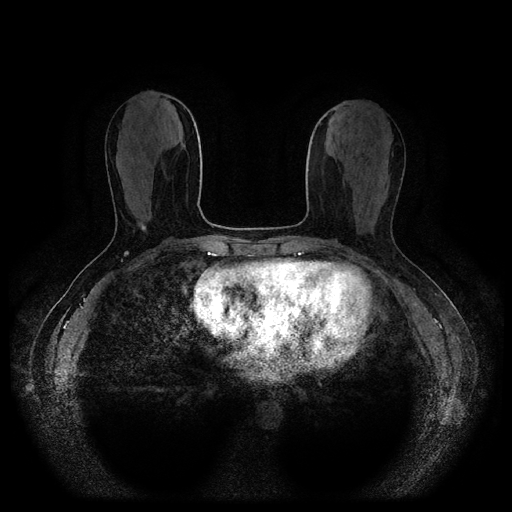
Breast MRI (dynamic contrast-enhanced, multi-phase), one axial slice. Slice 37 of 116 in the series (ordered by position). Dynamic contrast-enhanced series, time point 2 of 5 at this slice position (early post-contrast). 1.5 T. TE 2.6 ms, TR 5.3 ms. 2 mm slice thickness. 512 × 512 image matrix, field of view 360 × 360 mm. Patient: female, 53 years.
Structures marked on this image (semi-automatically segmented with operator editing):
- breast lesion (labelled 'tumour' in the annotation; benign lesions carry a separate 'benign' label): bounding box (x1, y1, x2, y2) in pixels: (137, 221, 146, 232)